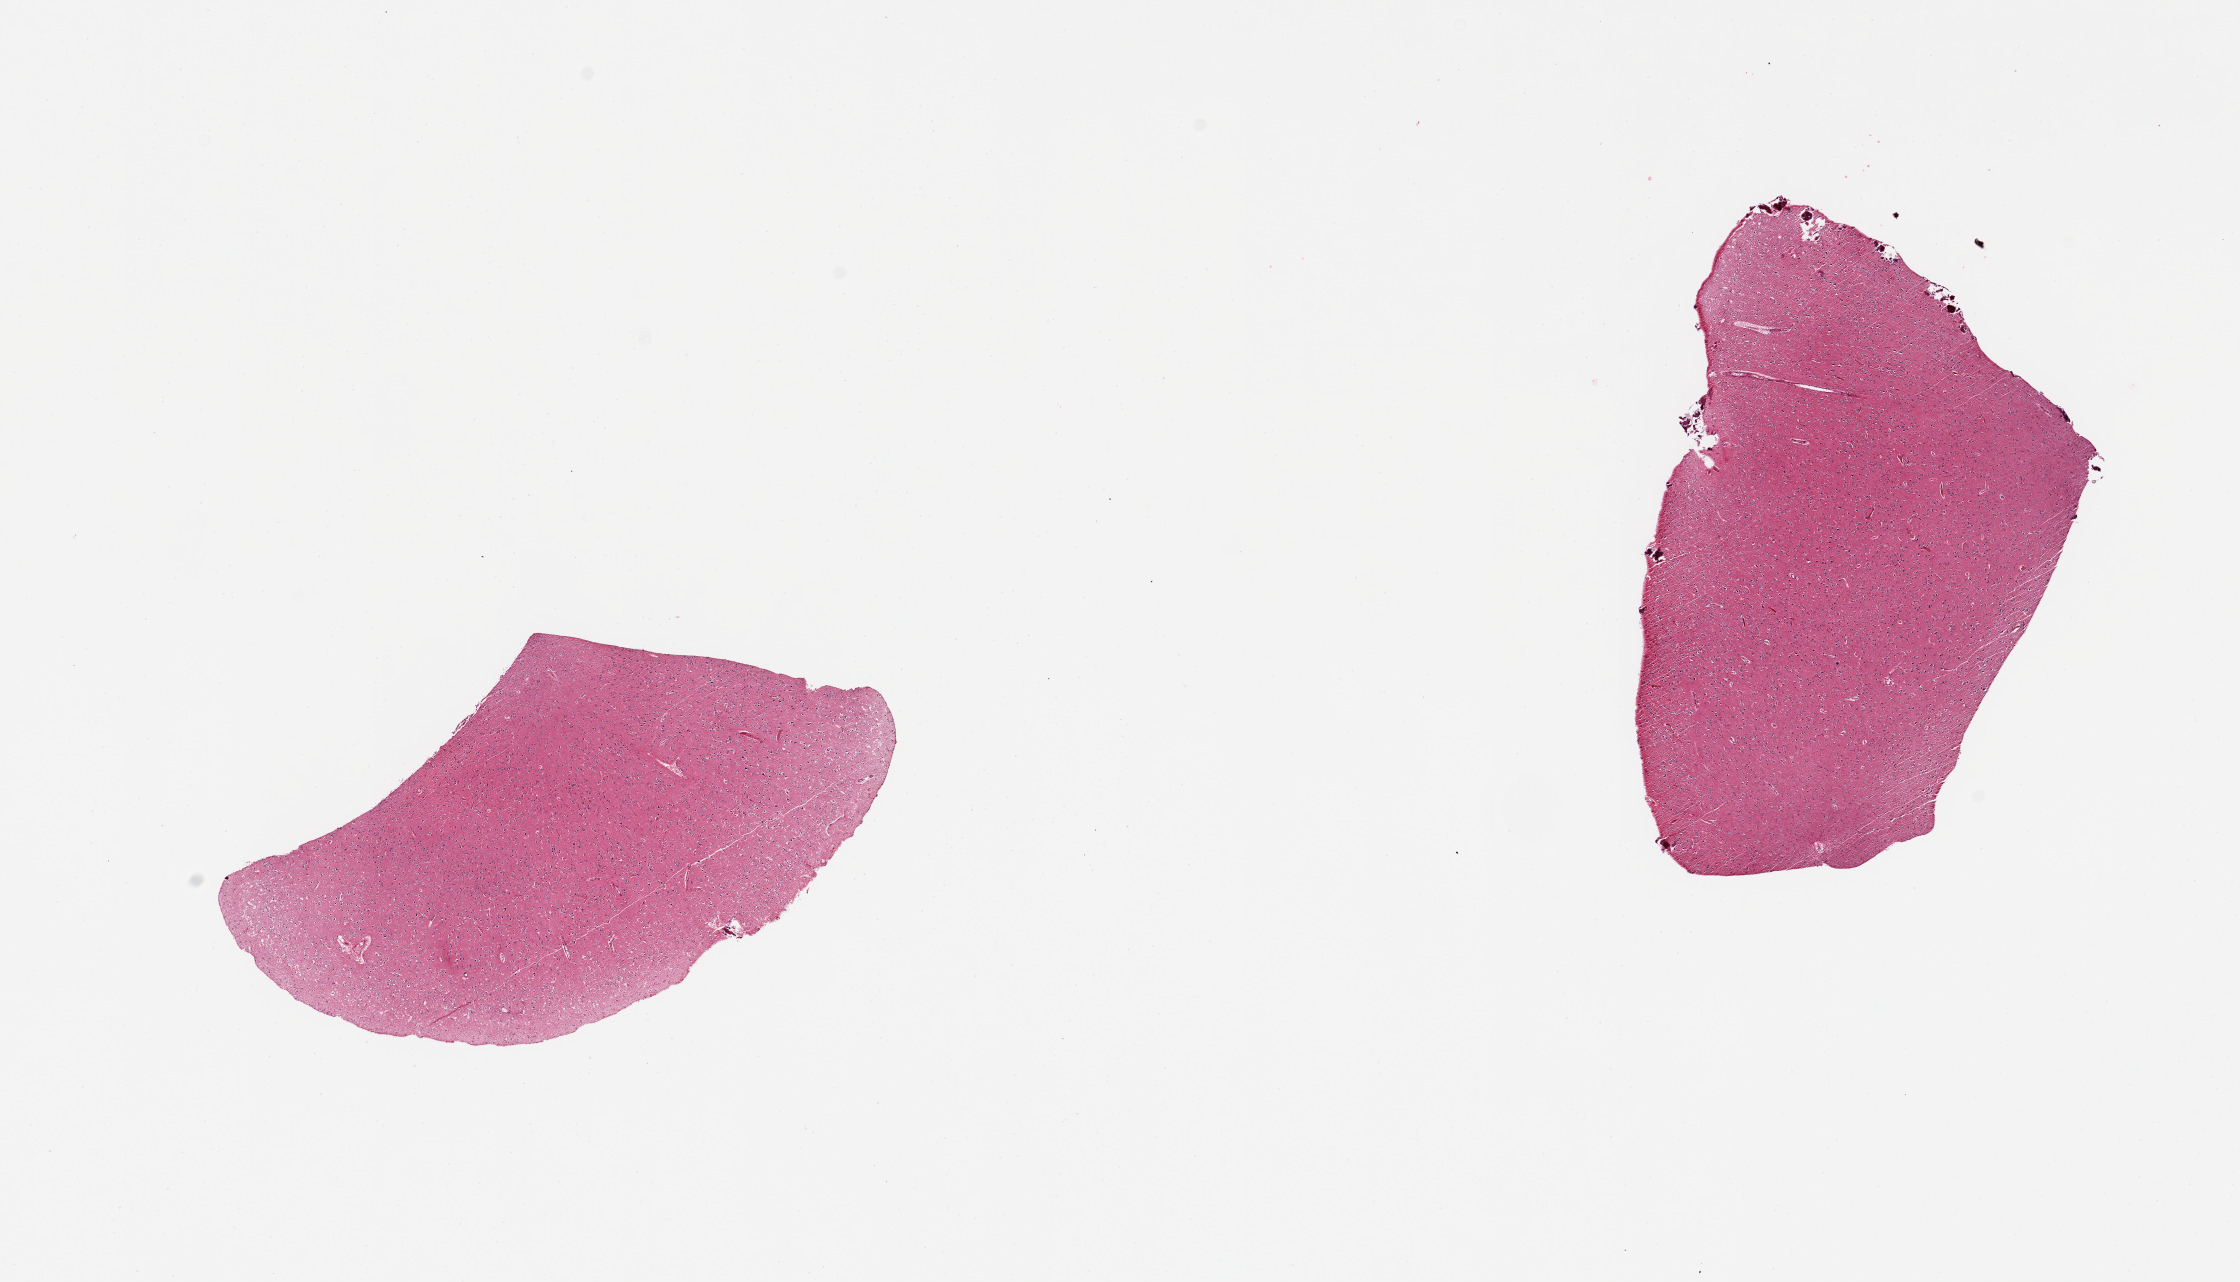
Digitized haematoxylin and eosin-stained section, brightfield — a low-resolution overview of the entire scanned area, about 17.7 x 10.1 mm. PAXgene-fixed paraffin-embedded (PFPE) section. Section of cerebral cortex (target tissue). Tissue donor sample.
* reviewer comment on this tissue sample: 2 pieces; cortex